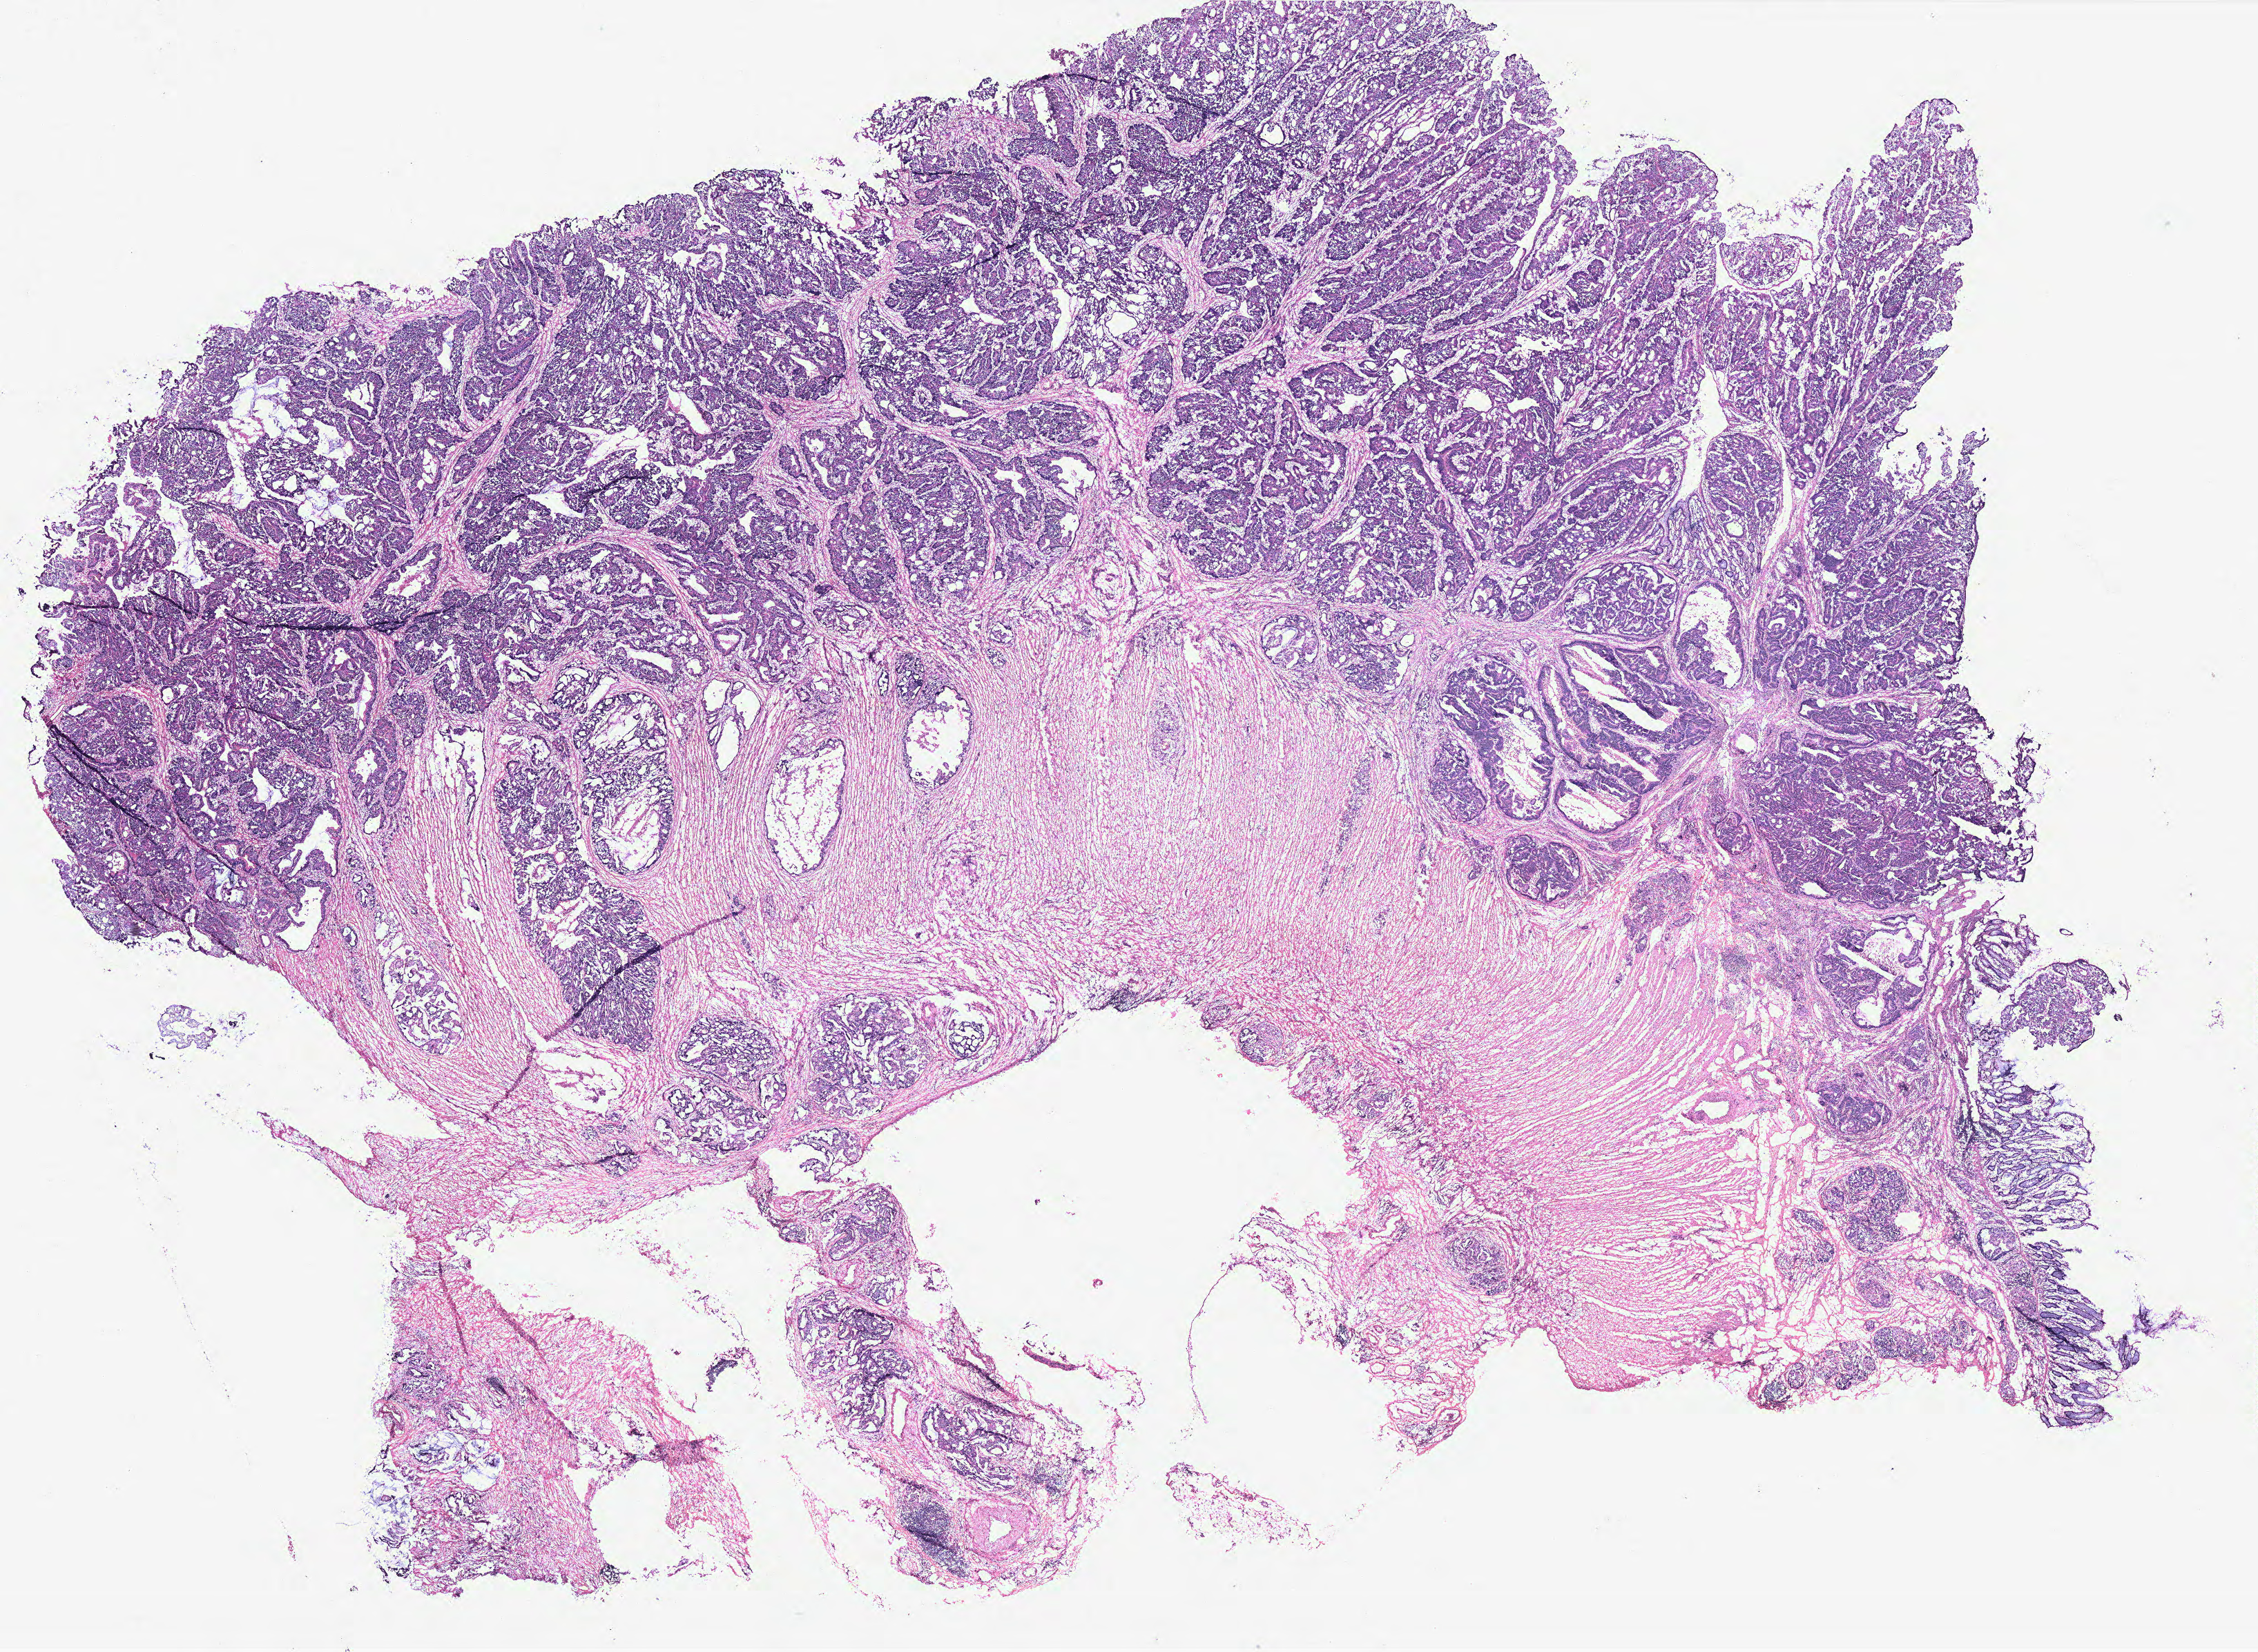
Digitized Hematoxylin and eosin (H&E) stained tissue section (whole slide) — whole scanned area (about 26.2 x 19.2 mm) shown as a low-resolution overview. Colon, tissue type not recorded.
Patient diagnosis (cohort enrolment): colon cancer (colon).